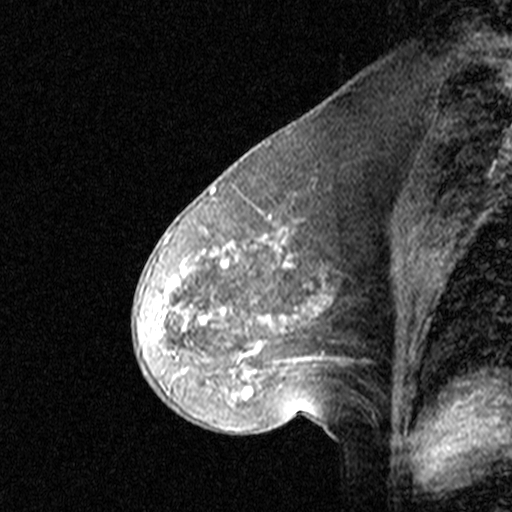
Breast MRI (dynamic contrast-enhanced), one sagittal slice; position 19 of 44 along the scan axis; dynamic contrast-enhanced study with each time point stored as its own series, time point 2 of 3 at this slice position (early post-contrast, ordered by acquisition time); 1.5 T; TE 4.5 ms, TR 11 ms; 3 mm slice thickness; 512 × 512 image matrix. Patient: female, 46 years. Case-level facts recorded for this patient, not image findings: setting: breast cancer imaged before/during neoadjuvant chemotherapy; receptor status: HER2-positive.
Structures marked on this image (semi-automatically segmented with operator editing):
- analysis volume of interest (the breast-tissue region the enhancement analysis was run in; not a lesion): box from (x=144, y=172) to (x=359, y=393) px
- tumour enhancement mask (voxels above the 90 % enhancement threshold inside the analysis volume of interest): (x=165, y=191)–(x=339, y=380)